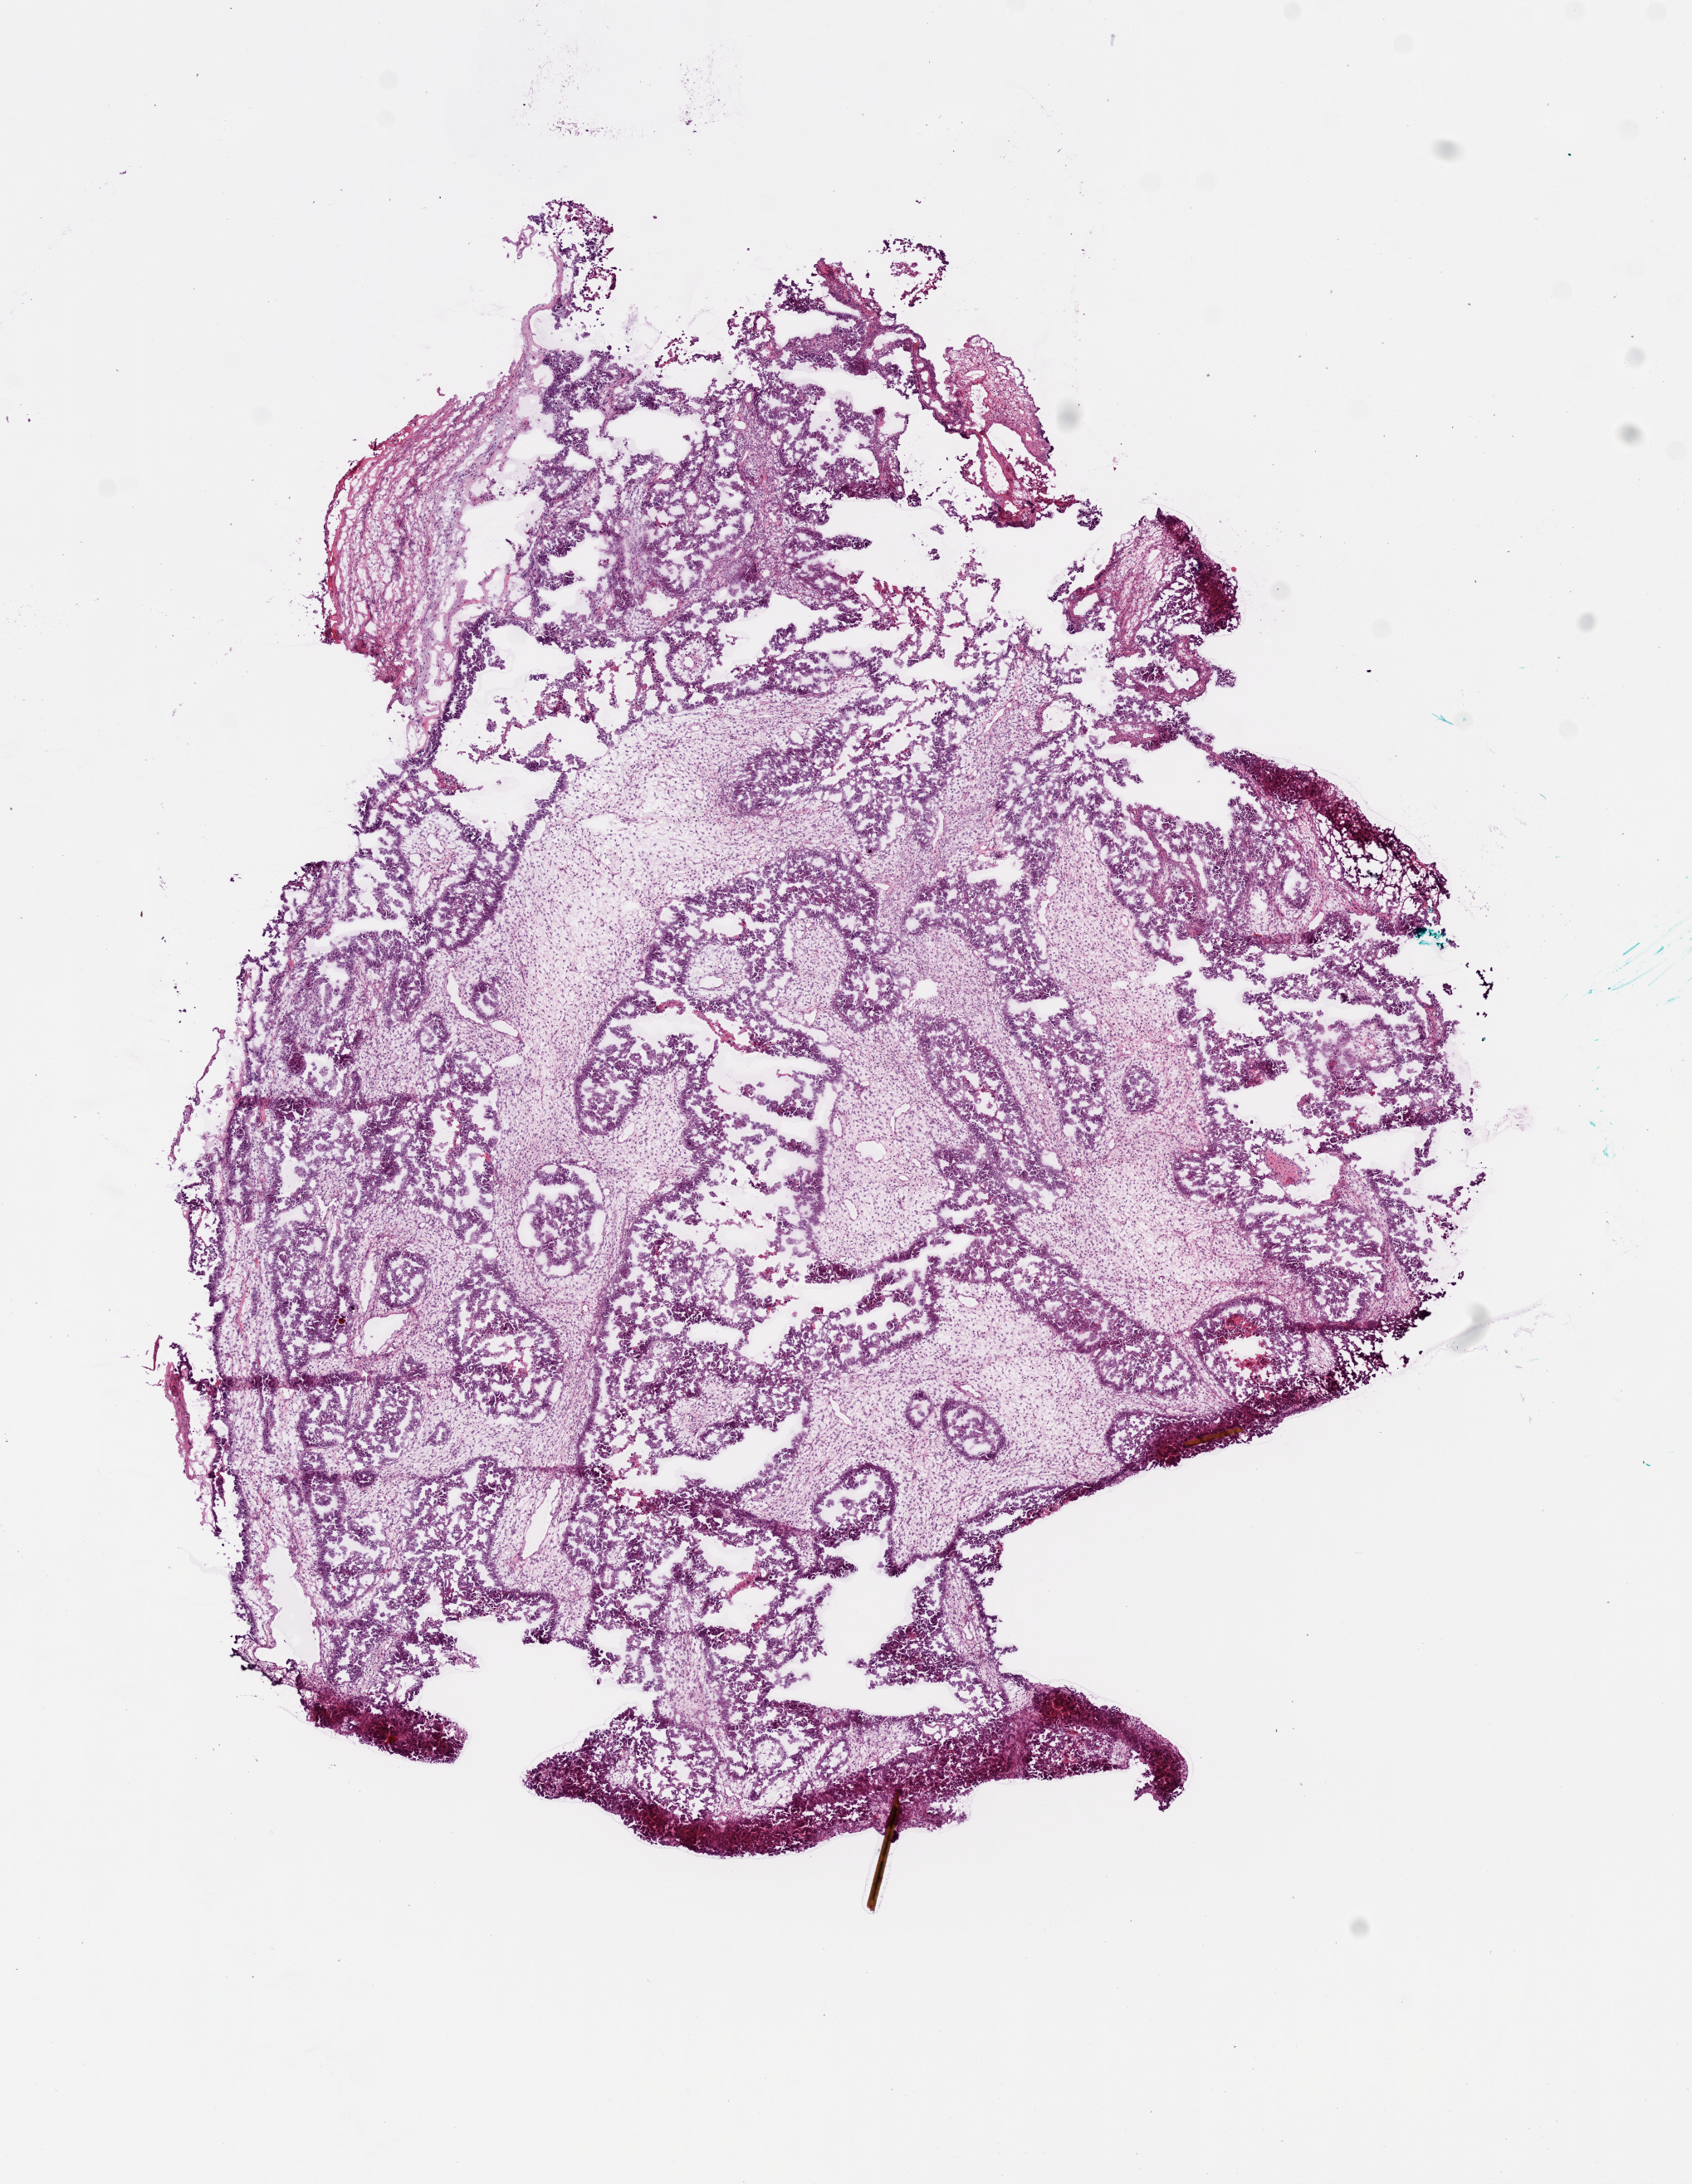
Whole-slide histology image, H&E — shown as a low-resolution overview of the whole scanned area (about 8.2 x 10.6 mm). Frozen section. Primary tumour sample from the ovary. Female, age 53 years at initial diagnosis. Histologic grade: G3 (poorly differentiated). Slide review estimates, as recorded: tumour cells 70%, tumour nuclei 85%, normal cells 0%, stromal cells 25%, necrosis 5%. Inflammatory infiltration, as recorded: lymphocyte infiltration 50%.
Diagnosis: Serous cystadenocarcinoma, NOS. FIGO stage: IV.